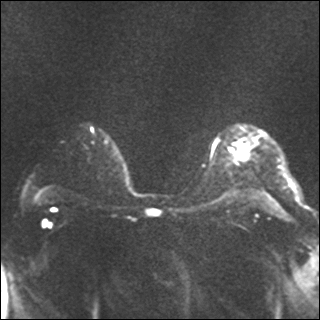
Breast MRI, one axial slice. Position 24 of 35 along the scan axis. Diffusion-weighted series; image 2 of 4 stored at this slice position (different b-values; order by instance number). 1.5 T. 320 × 320 image matrix. Female patient.
Outlined on this slice (outlined manually by an expert reader):
- tumour on diffusion-weighted imaging: bounding box [x1, y1, x2, y2] px = [240, 146, 245, 153]